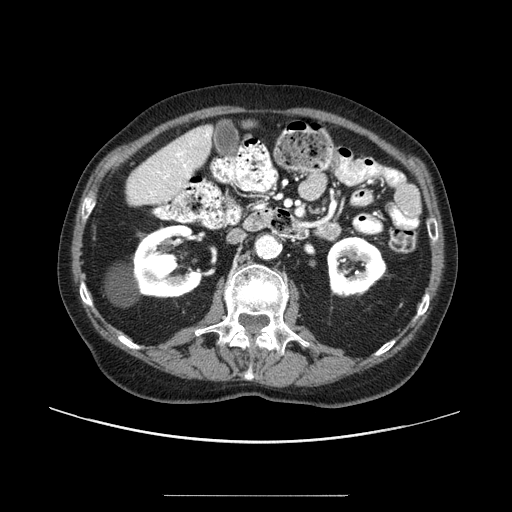
Contrast-enhanced abdominal CT (liver protocol), one axial slice; slice 31 of 91 in the series (ordered by position); reconstruction kernel STANDARD; 100 kVp; one of 2 acquisitions stored at this slice position; soft-tissue window (W 400 / L 40 HU); 2.5 mm slice thickness; 512 × 512 image matrix, field of view 400 × 400 mm. From the clinical record (not read from this slice): diagnosis: hepatocellular carcinoma (patient treated with transarterial chemoembolisation; whether this scan precedes or follows treatment is not stated here); TNM stage (as recorded): Stage-I; Child-Pugh class: A; tumour differentiation: moderately differentiated; tumour nodularity: uninodular.
Annotated regions visible in this slice (semi-automatic segmentation, software-assisted and operator-edited):
- liver parenchyma outside the tumour (the mass and vessels are separate outlines, so this box may not span the whole liver): bounding box (x1, y1, x2, y2) in pixels: (126, 125, 212, 204)
- liver vessels: (146, 131, 209, 198)